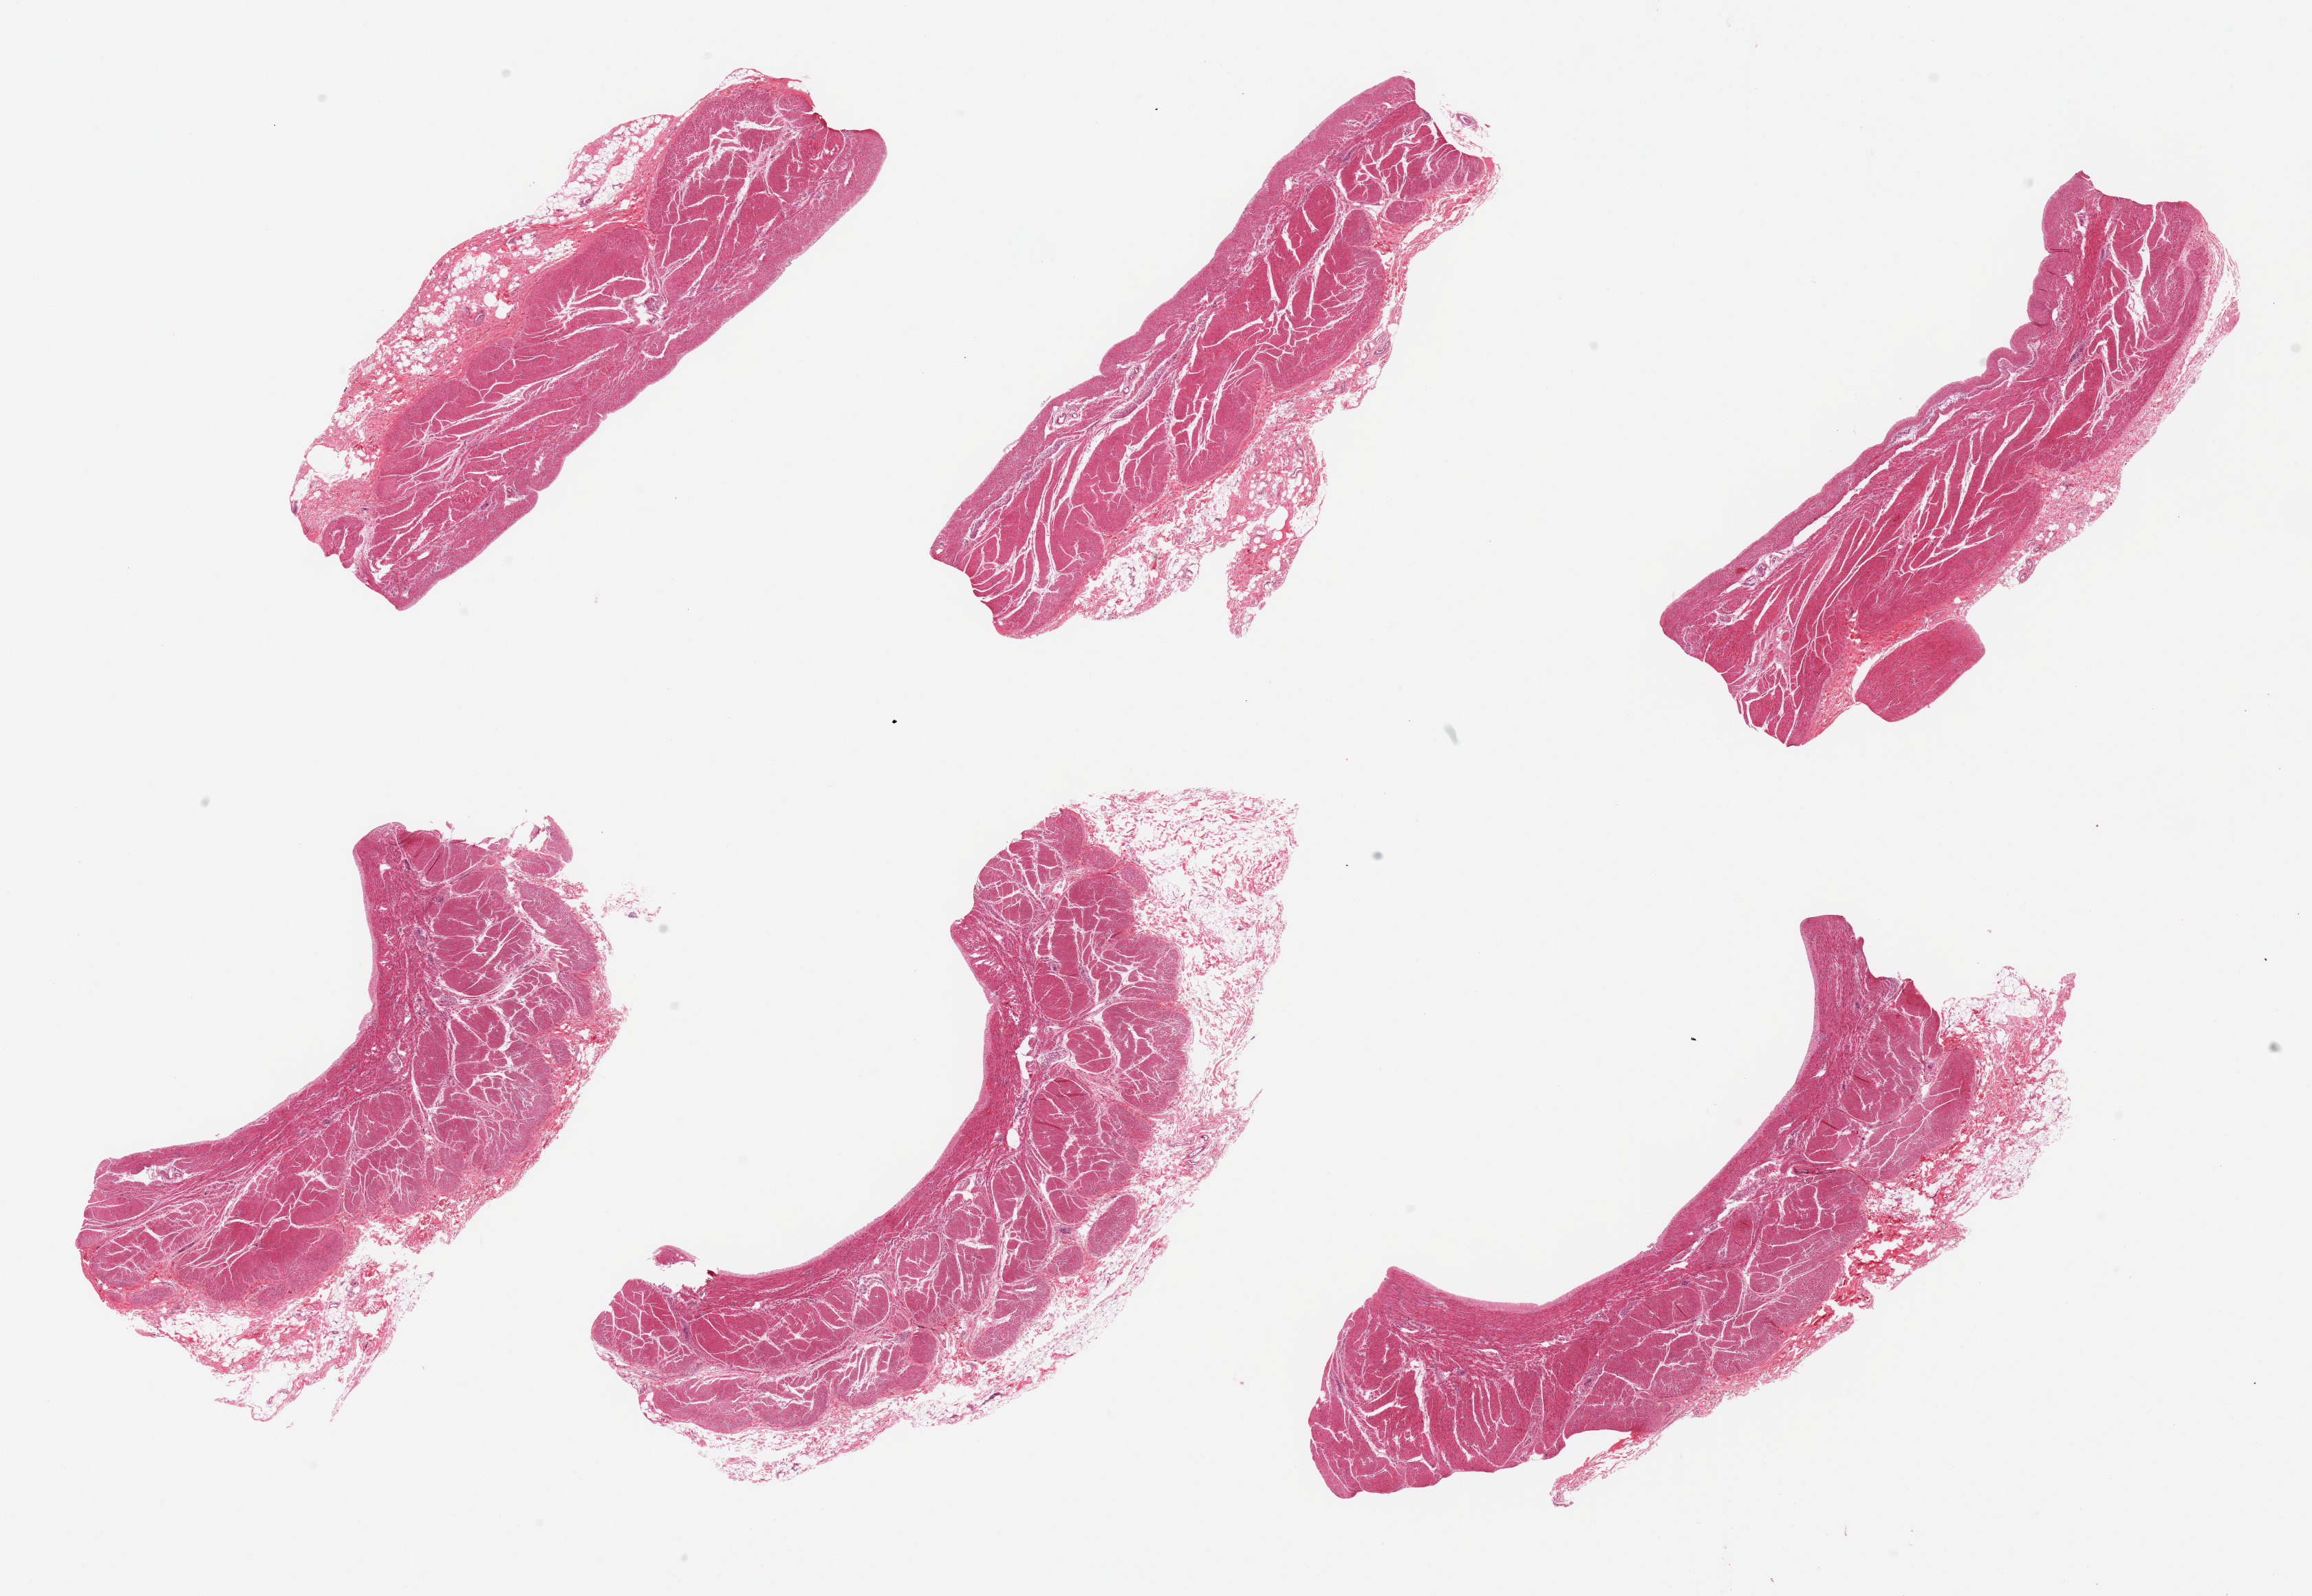
Hematoxylin and eosin (H&E) whole-slide image, whole scanned area (about 26.6 x 18.3 mm, from a 20x scan) shown as a low-resolution overview, PAXgene-fixed paraffin-embedded (PFPE) section, target tissue: stomach, donor tissue sample. Donor sex: female.
Pathologist's review note for this sample: 6 pieces; muscularis propria only, no mucosa.